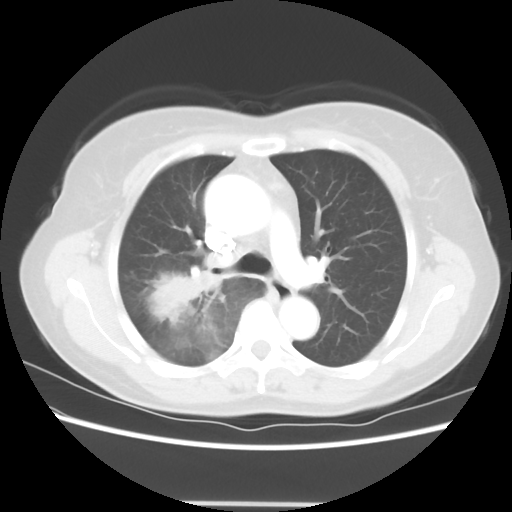
Chest CT, one axial slice; position 39 of 56 along the scan axis; 120 kVp; lung window (W 1500 / L -600 HU); 5 mm slice thickness; 512 × 512 image matrix, field of view 360 × 360 mm. Patient: female, 55 years. From the clinical record (not read from this slice): clinical TNM (as recorded): T2 N1 M0; histopathological grade: G2-3.
Annotated regions visible in this slice (bounding box drawn by a radiologist):
- lung tumour (recorded histology: adenocarcinoma): bounding box <137,256,231,336> (left, top, right, bottom; pixels)